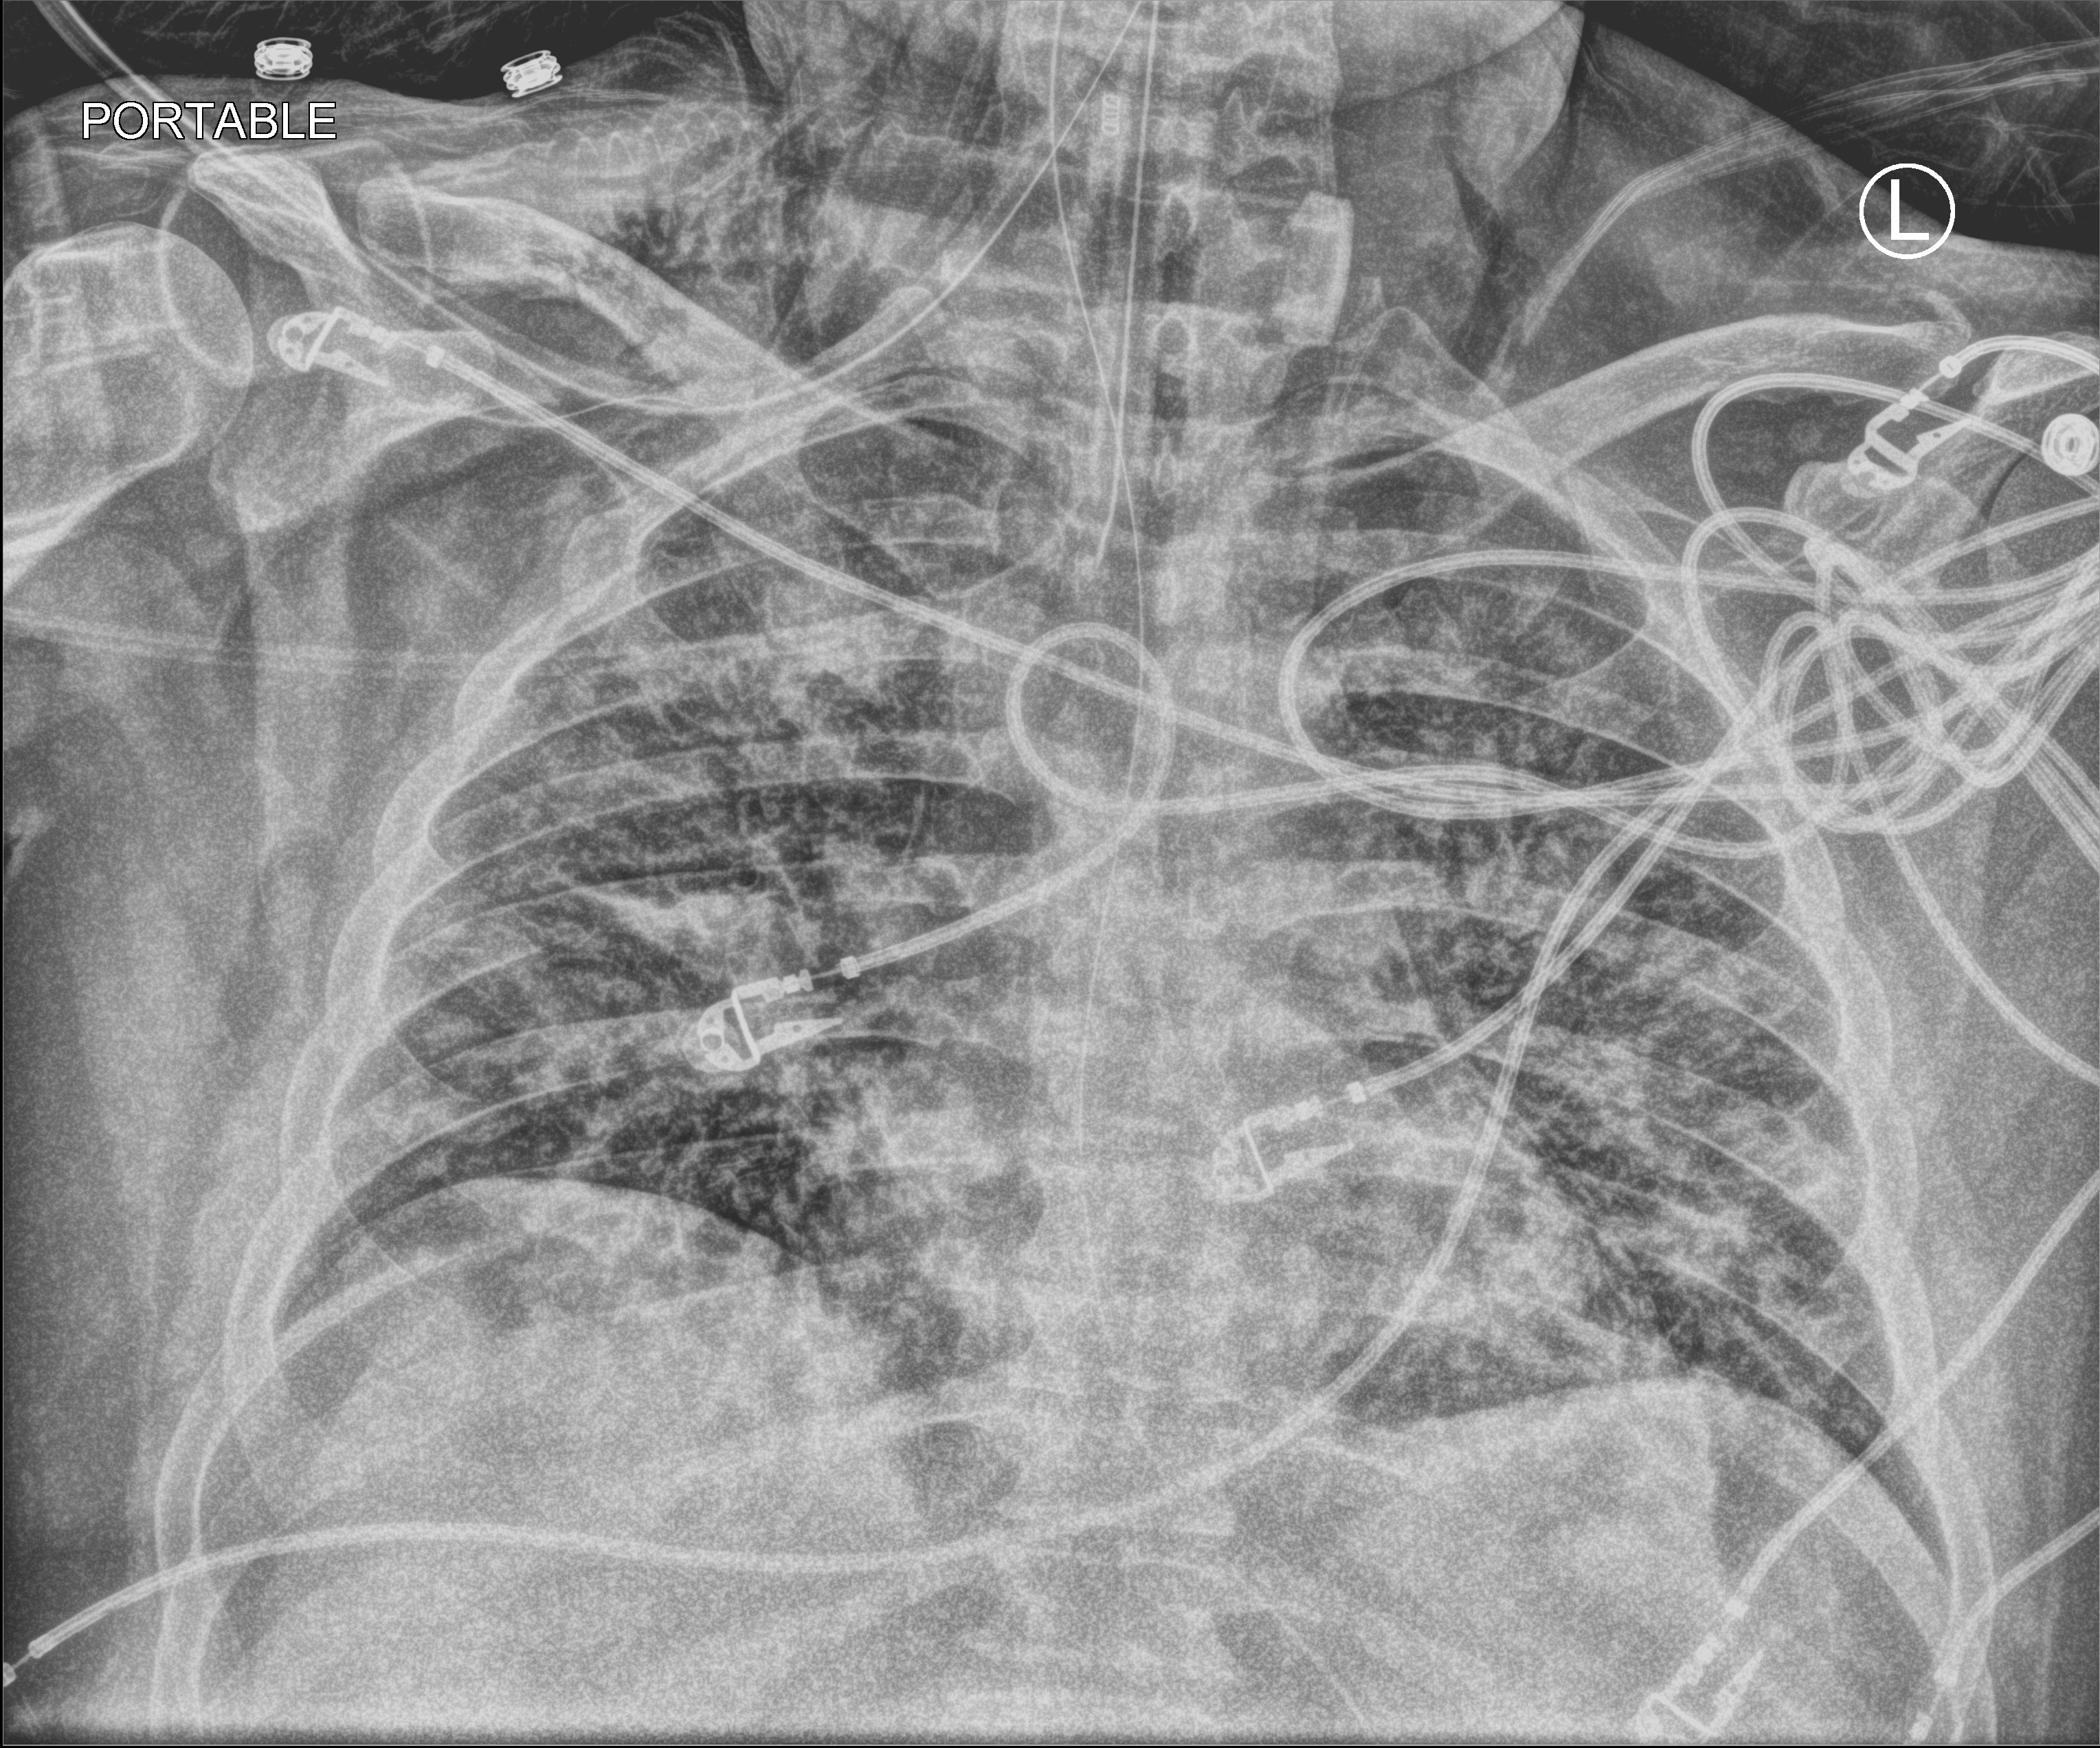
Bedside chest radiograph (computed radiography), anteroposterior (AP) projection. Adult patient hospitalised with COVID-19, age 18–59 years.
From the hospital-stay record, not from the radiograph (when in the stay this image was taken is not recorded): admitted to intensive care during this hospital stay: yes.